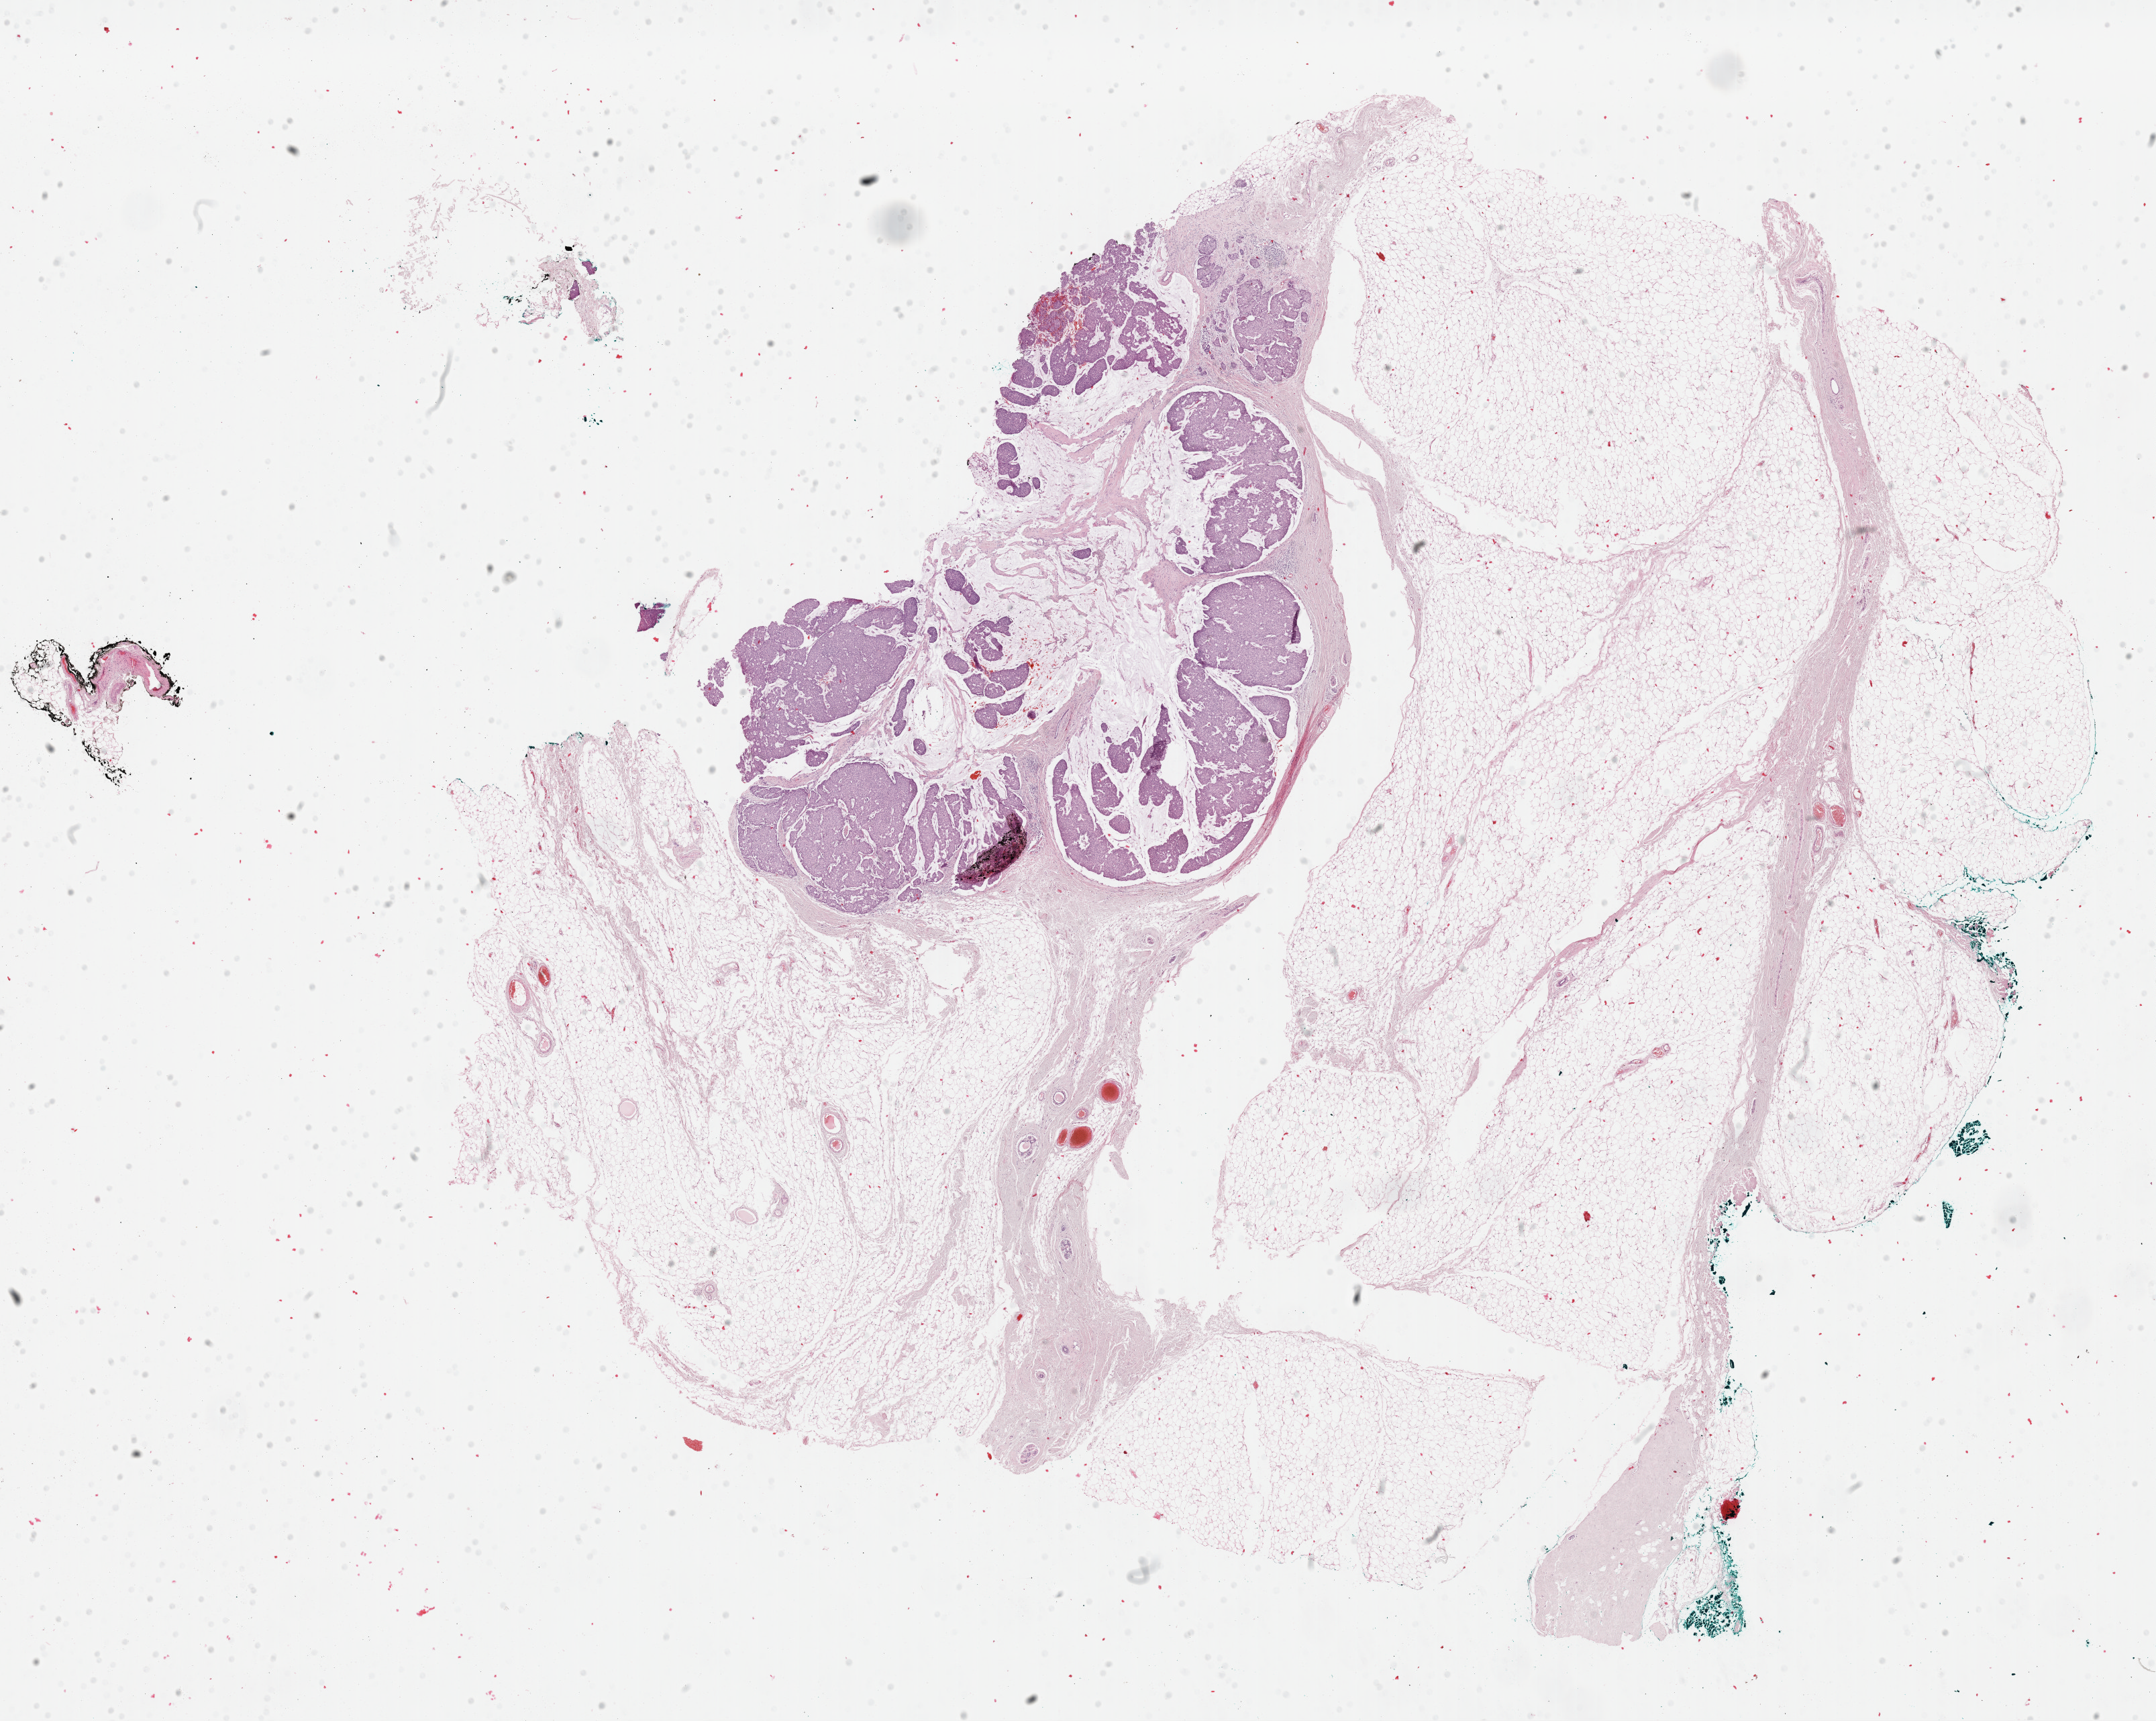
H&E whole-slide image, a low-resolution overview of the entire scanned area, about 25.4 x 20.3 mm (from a 40x scan); formalin-fixed paraffin-embedded (FFPE) diagnostic section; sample: primary tumour, breast. Female patient; age at initial diagnosis 66 years.
Lymph nodes positive (case pathology): 0 of 1 examined. AJCC pathologic stage: IA (7th edition). Histologic diagnosis: Infiltrating duct mixed with other types of carcinoma.